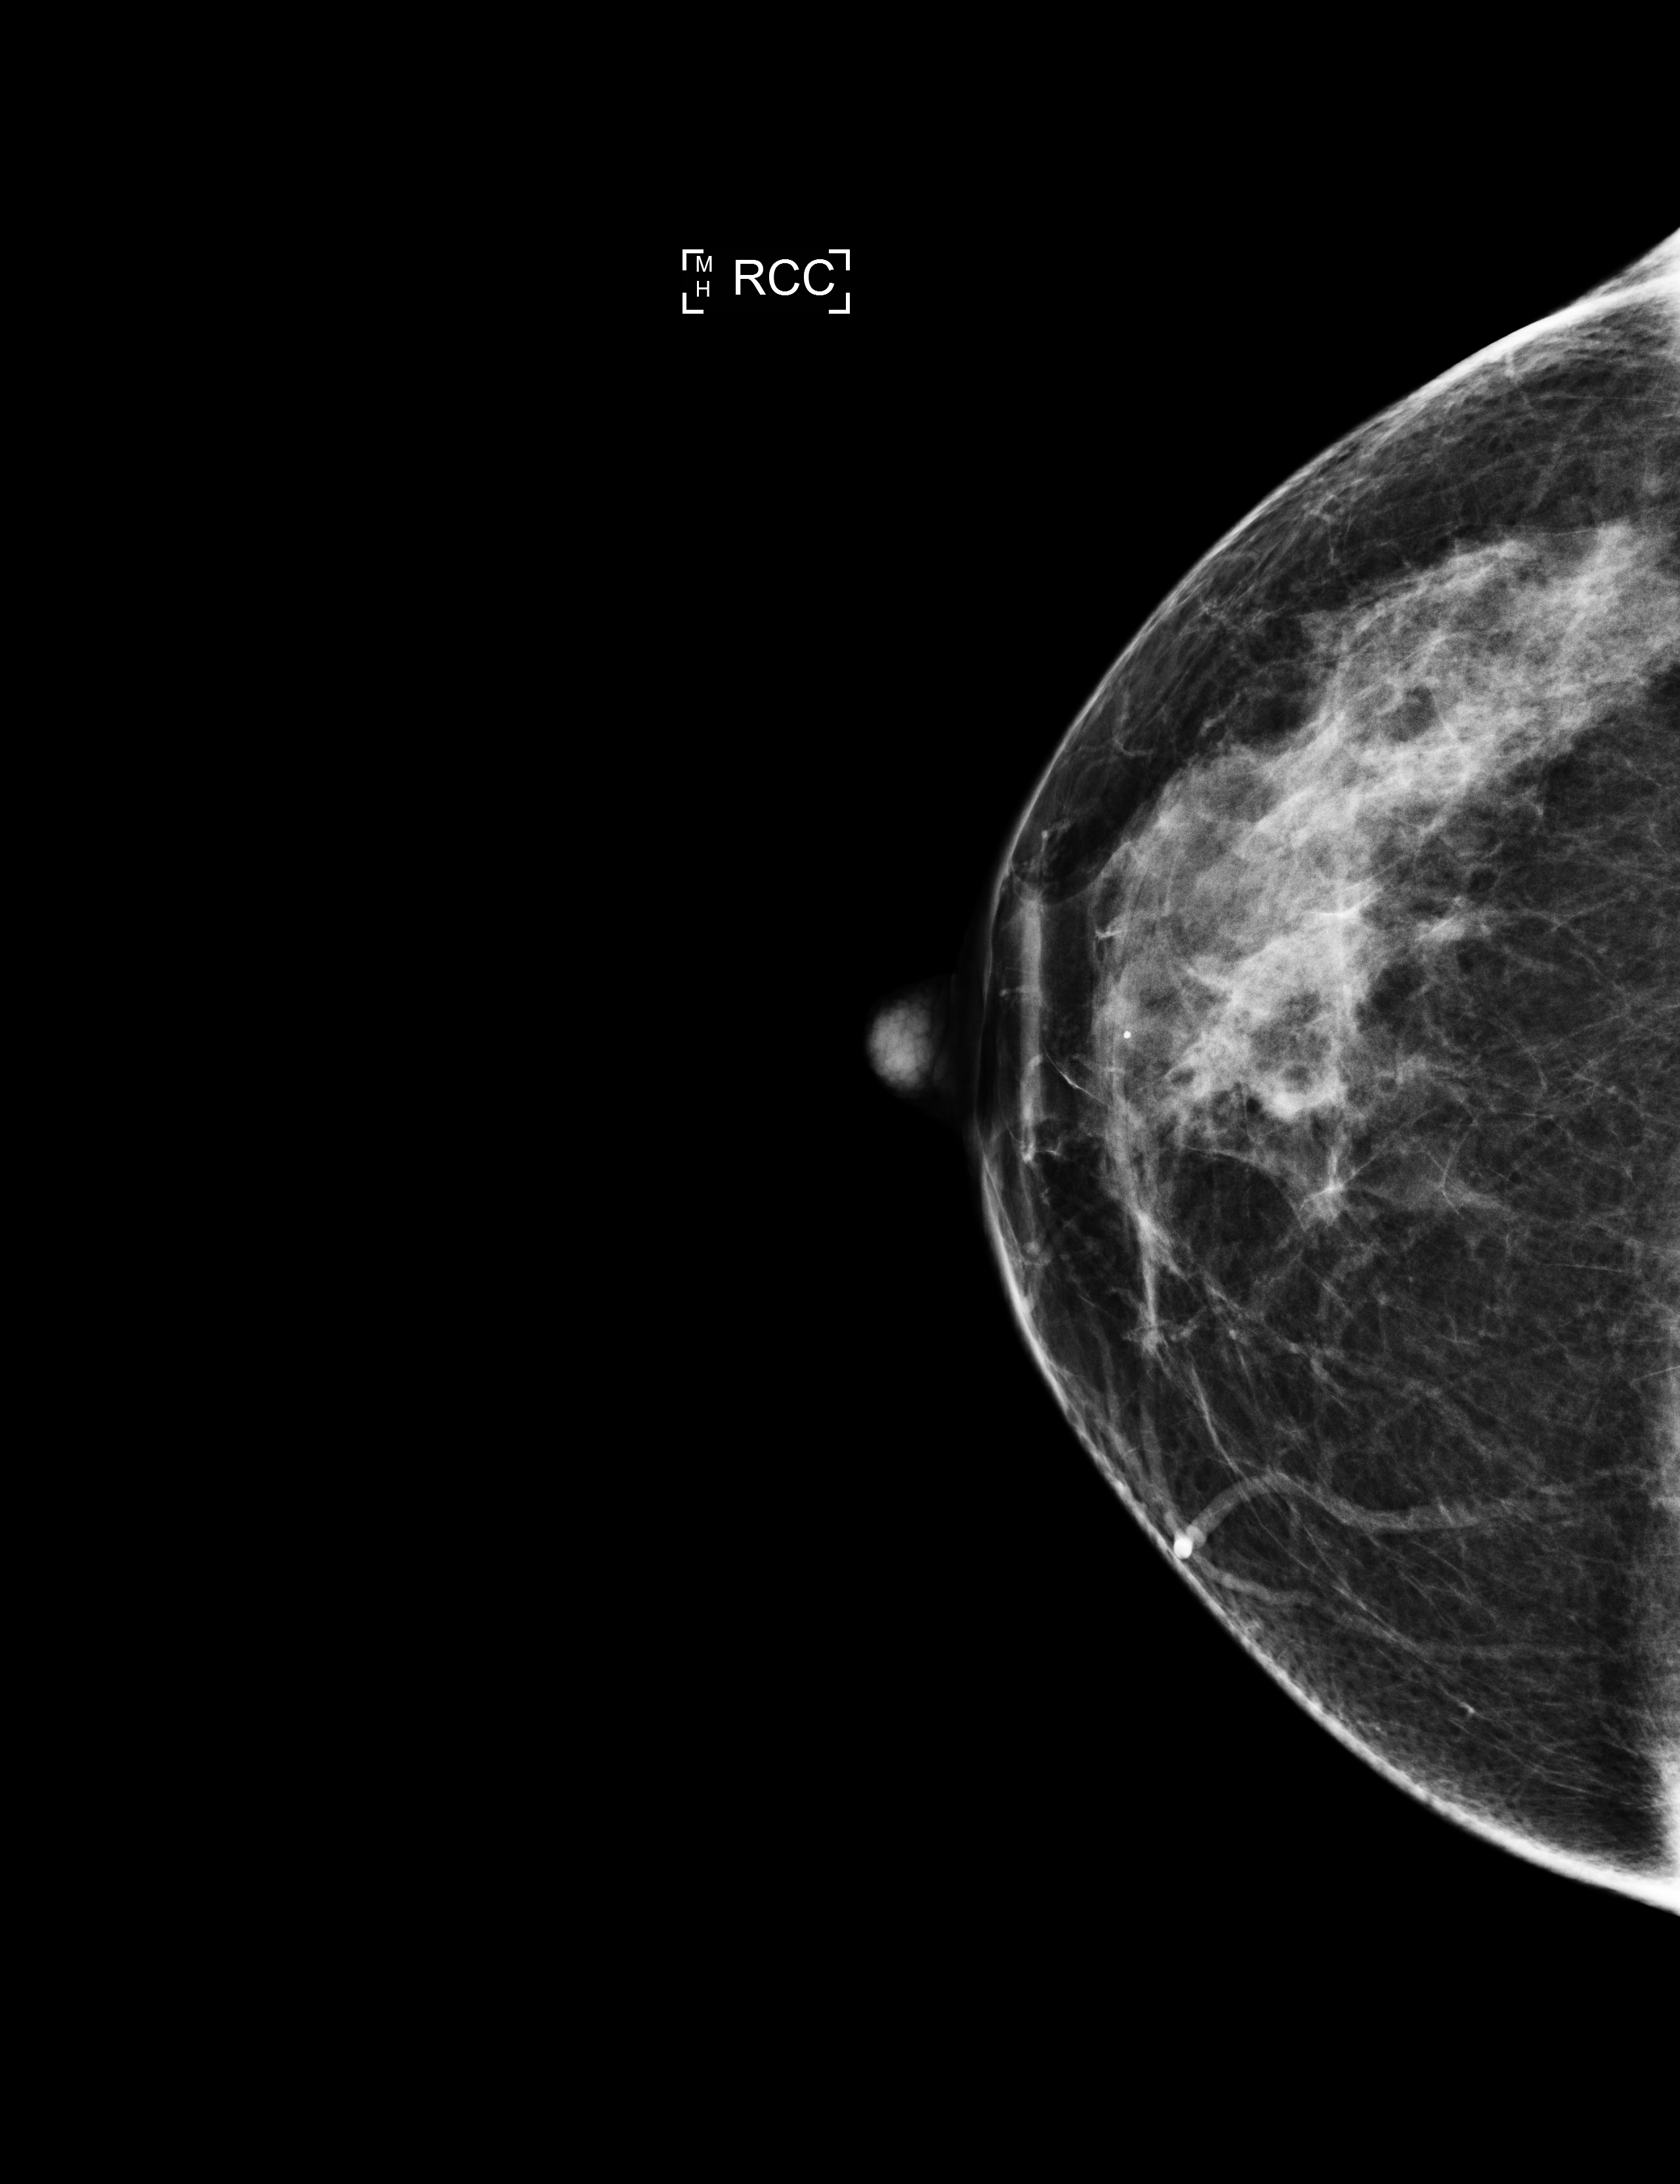
Full-field digital mammogram (FFDM), right breast, CC view, annual screening mammography examination. Female patient, age 51 years.
- breast density at the screening exam (both breasts): heterogeneously dense (BI-RADS density category c)
- final BI-RADS category for the screening round (tomosynthesis exam, both breasts): category 1
- recall: no recall after this screen